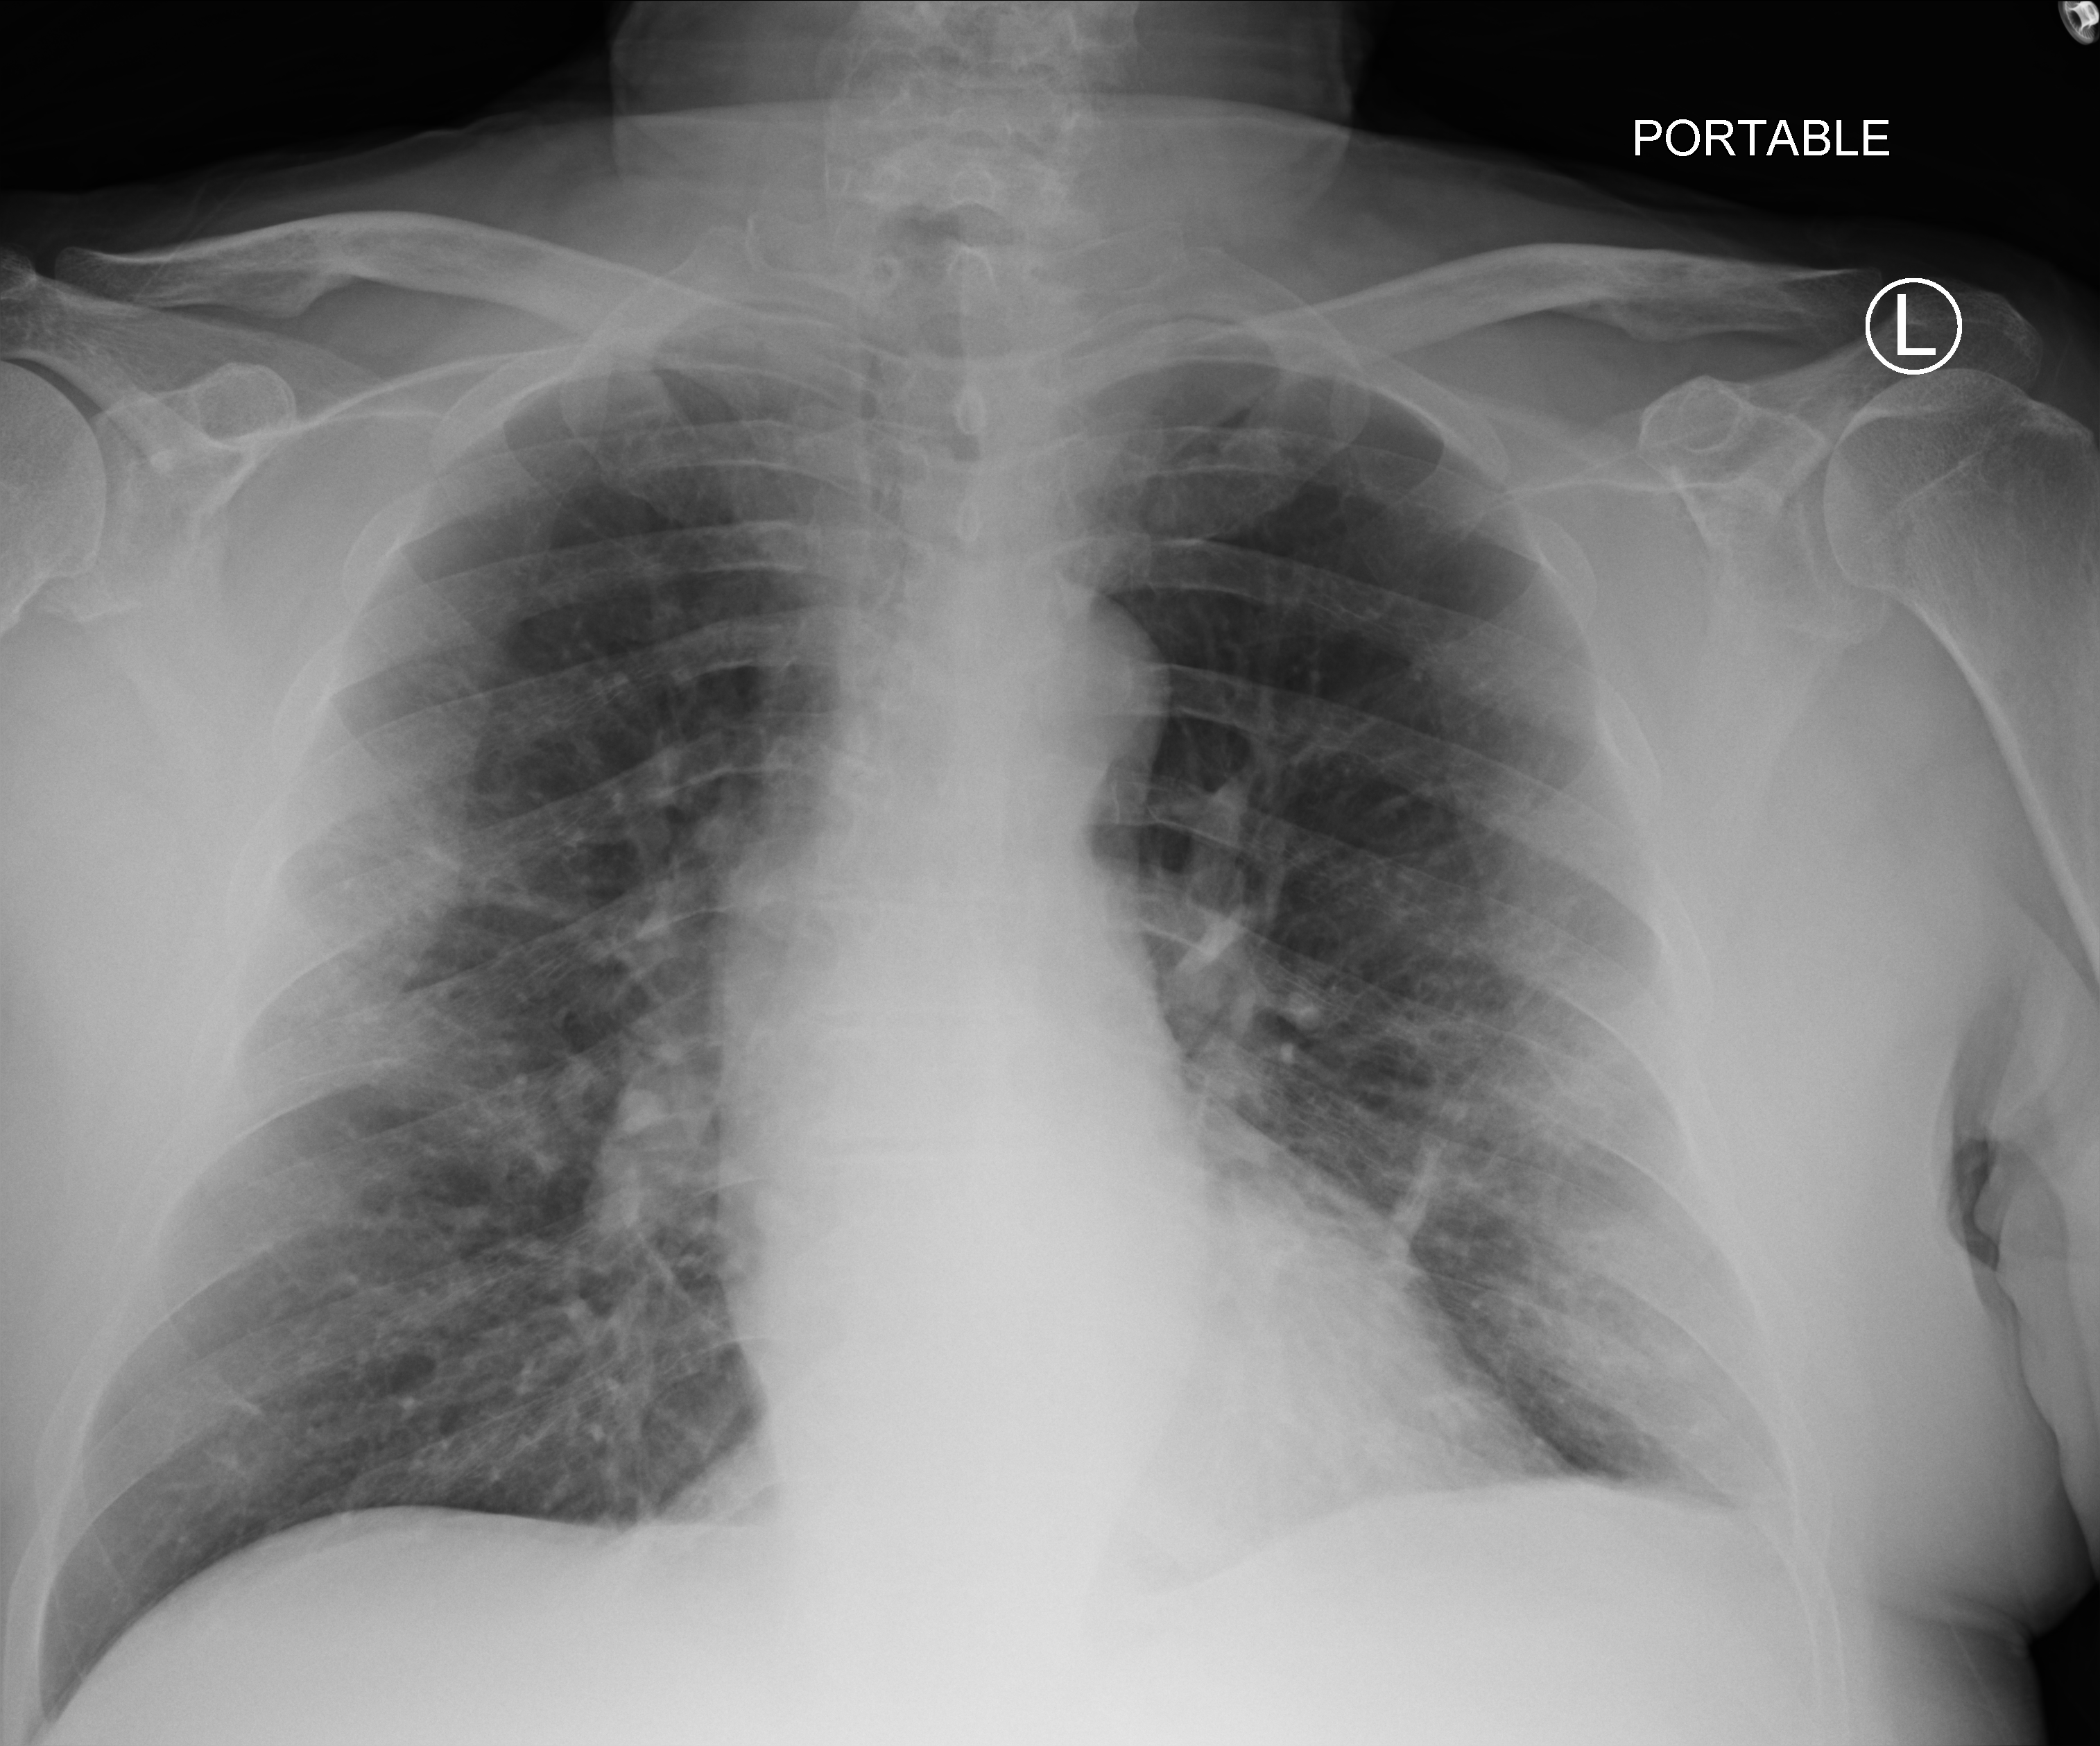
Bedside chest radiograph (computed radiography). Patient hospitalised with COVID-19; male, aged 60–74 years.
Hospital-stay facts (about this admission, not read from this image; timing relative to this image not recorded):
- mechanically ventilated during this hospital stay: yes
- admitted to intensive care during this hospital stay: yes